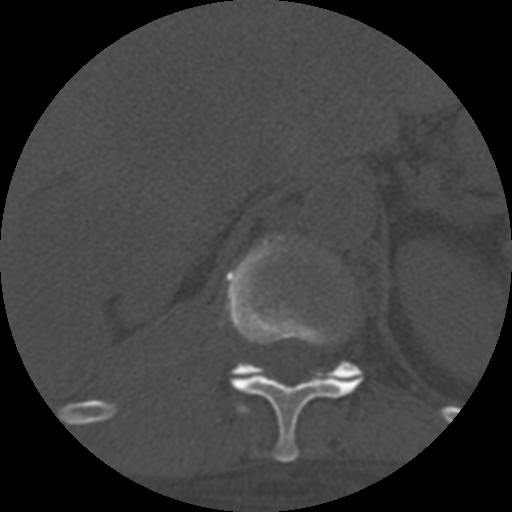
CT including the spine, one axial slice. Position 328 of 708 along the scan axis. Reconstruction kernel STANDARD. 120 kVp. One of 3 acquisitions stored at this slice position. Bone window (W 1800 / L 400 HU). 1.25 mm slice thickness. 512 × 512 image matrix, field of view 160 × 160 mm. Patient age 55 years. From the clinical record (not read from this slice): primary cancer: colon.
Structures marked on this image (semi-automatically segmented with operator editing):
- T11 vertebra: box from (x=224, y=235) to (x=362, y=463) px
- T12 vertebra: (x=231, y=361)–(x=363, y=380)